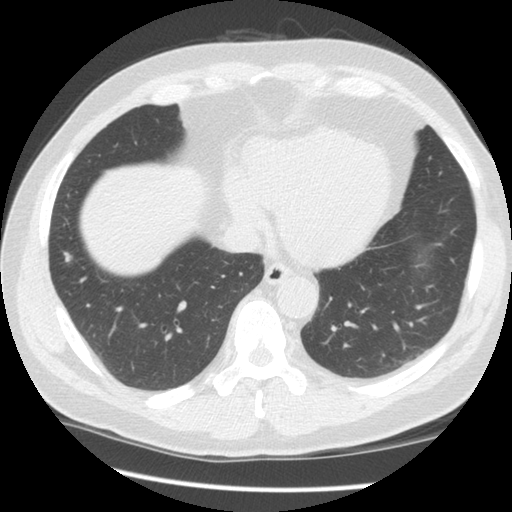
Low-dose screening chest CT, axial slice. Second annual screen. Lung window (W 1500 / L -600 HU). 2.5 mm slice thickness. Standard (soft-tissue) reconstruction kernel (STANDARD). Male, age 61 years at enrolment. Current smoker at enrolment.
Expert reader's lesion annotation, bounding box [x1, y1, x2, y2] px = [47, 241, 87, 279]. Reader record for this screening exam (exam-level; its link to the box is not recorded): non-calcified nodule or mass ≥4 mm, right lower lobe, 5 × 4 mm, smooth margins, soft tissue attenuation, pre-existing on the prior screen: no. Official screen result: positive, other.